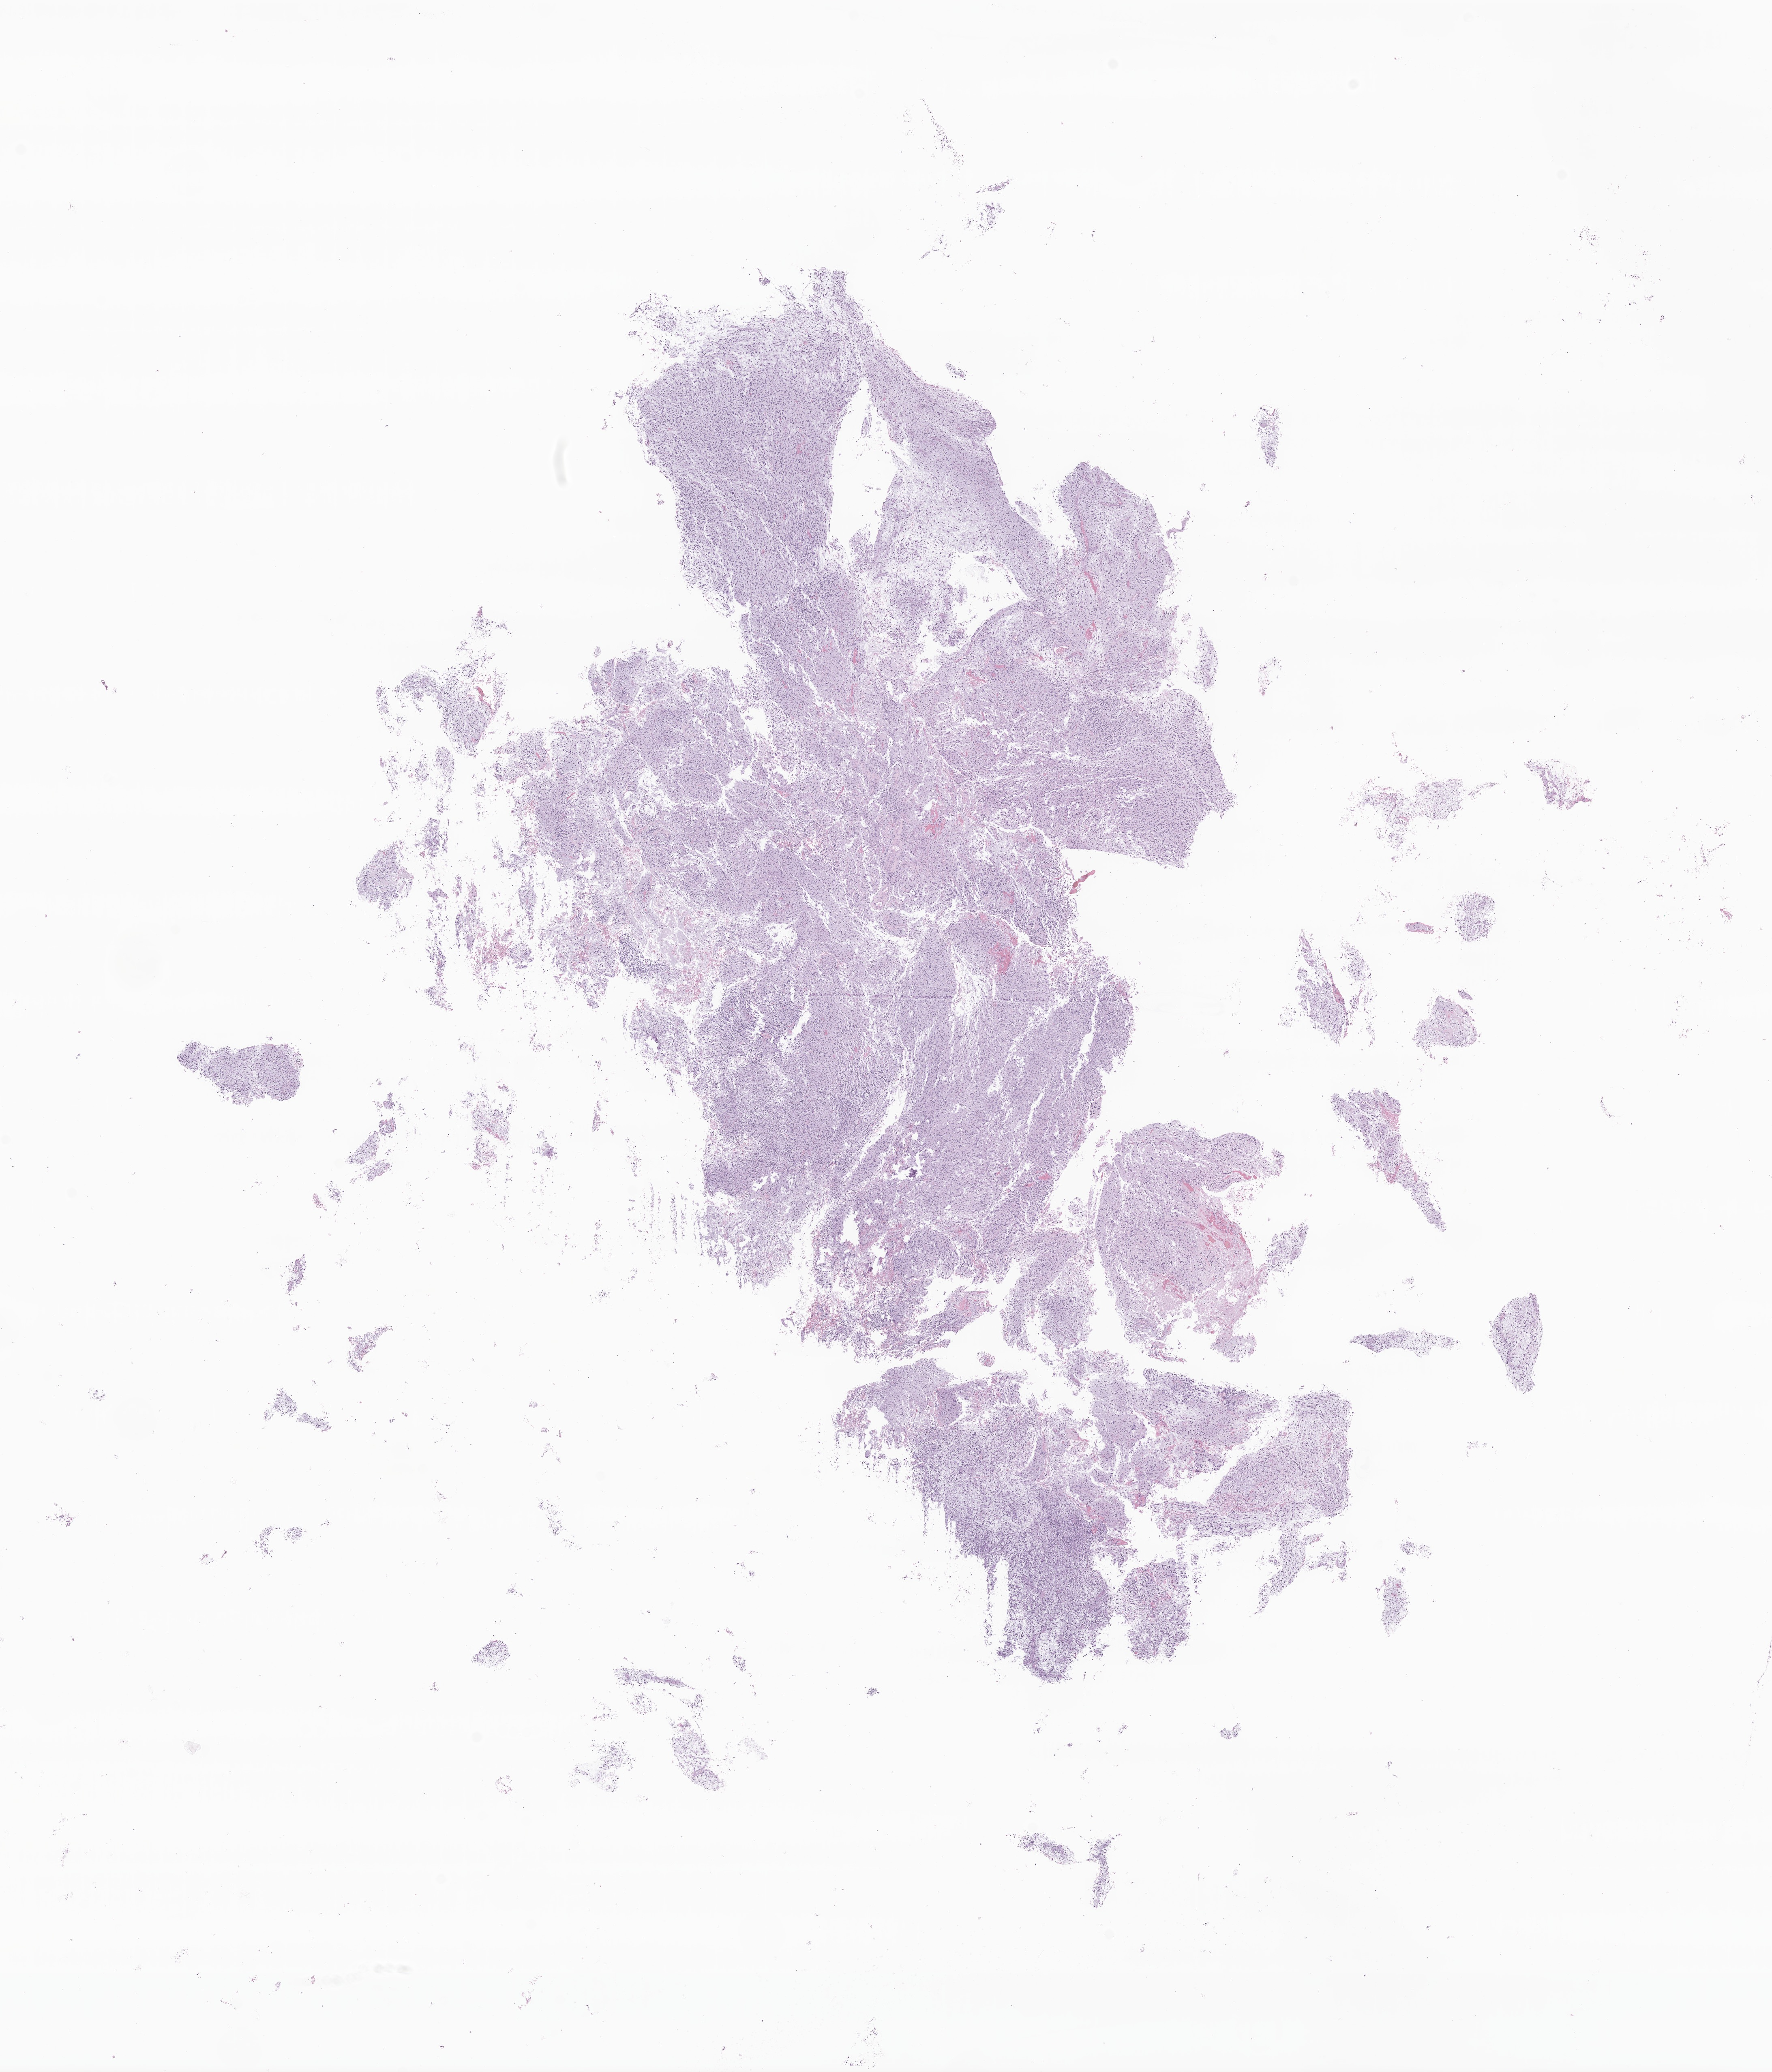
Digitized hematoxylin and eosin (H&E)-stained section of tumor tissue from the brain stem — a low-resolution overview of the entire scanned area, about 18.4 x 21.5 mm, FFPE section. Patient male; age 151 months.
Diagnosis: Glioma, malignant.